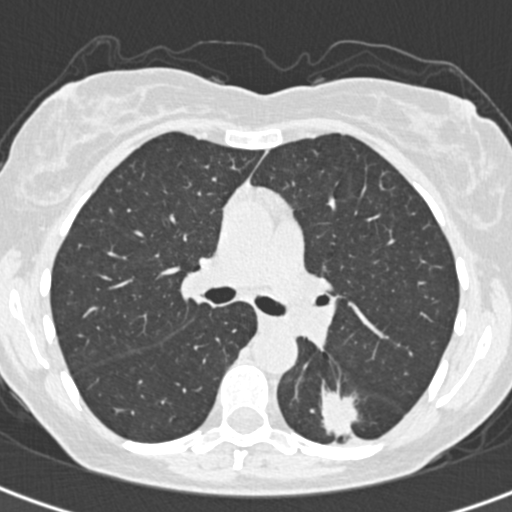
Low-dose screening chest CT, one axial slice. Position 206 of 328 along the scan axis. 120 kVp. Lung window (W 1500 / L -600 HU). 1 mm slice thickness. 512 × 512 image matrix.
Outlined on this slice (expert manual segmentation):
- lesion 1 (tumor, lower lobe of left lung): bounding box <321,388,358,437> (left, top, right, bottom; pixels)